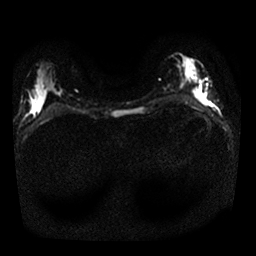
Breast MRI, one axial slice. Position 9 of 25 along the scan axis. Diffusion-weighted series; image 2 of 4 stored at this slice position (different b-values; order by instance number). 1.5 T. 4 mm slice thickness. 256 × 256 image matrix. Female patient.
Outlined on this slice (manually delineated by an expert):
- tumour on diffusion-weighted imaging: bounding box <194,85,201,98> (left, top, right, bottom; pixels)